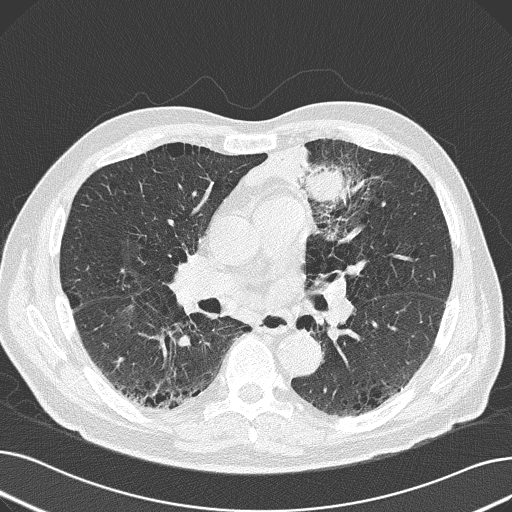
Chest CT (low-dose screening protocol), one axial image, baseline screening round, lung window (W 1500 / L -600 HU), 512 × 512 image matrix, field of view 370 × 370 mm. Male, age 69 years at enrolment. Former smoker at enrolment.
• Expert-annotated lung lesion, bounding box (x1, y1, x2, y2) in pixels: (240, 125, 388, 248).
• The exam's reader record, not a measurement of the box and not confirmed to be the same lesion: non-calcified nodule or mass ≥4 mm, left upper lobe, 6 × 10 mm, spiculated (stellate) margins, soft tissue attenuation.